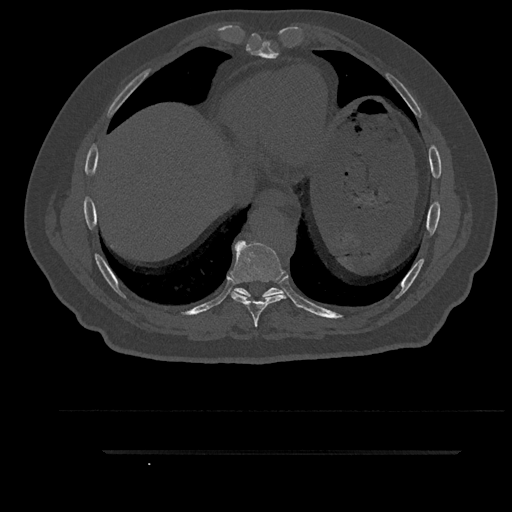
CT including the spine, one axial slice; position 457 of 797 along the scan axis; 120 kVp; bone window (W 1800 / L 400 HU); 0.5 mm slice thickness; 512 × 512 image matrix. Male patient, age 63 years. From the clinical record (not read from this slice): primary cancer: renal.
Structures marked on this image (semi-automatic segmentation, software-assisted and operator-edited):
- T8 vertebra: bounding box [x1, y1, x2, y2] px = [231, 241, 286, 327]
- T9 vertebra: [233, 288, 283, 298]